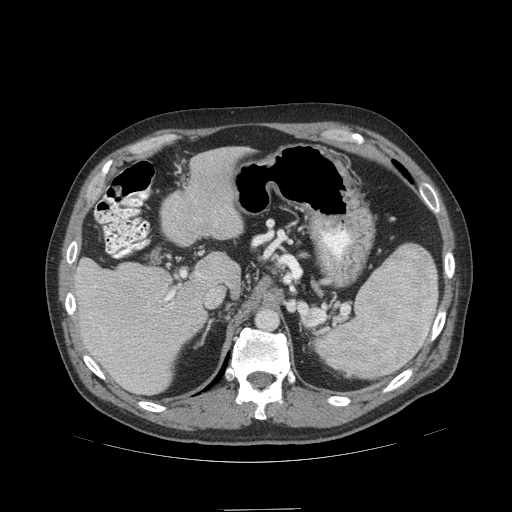
Contrast-enhanced abdominal CT (liver protocol), one axial slice; slice 68 of 99 in the series (ordered by position); reconstruction kernel STANDARD; soft-tissue window (W 400 / L 40 HU); 2.5 mm slice thickness; 512 × 512 image matrix, field of view 440 × 440 mm. From the clinical record (not read from this slice): diagnosis: hepatocellular carcinoma (patient treated with transarterial chemoembolisation; whether this scan precedes or follows treatment is not stated here); TNM stage (as recorded): Stage-I; Child-Pugh class: A; tumour nodularity: uninodular; tumour size: 3.6 cm.
Structures marked on this image (semi-automatic segmentation, software-assisted and operator-edited):
- liver parenchyma outside the tumour (the mass and vessels are separate outlines, so this box may not span the whole liver): bounding box (x1, y1, x2, y2) in pixels: (72, 146, 247, 394)
- liver vessels: (93, 272, 202, 351)